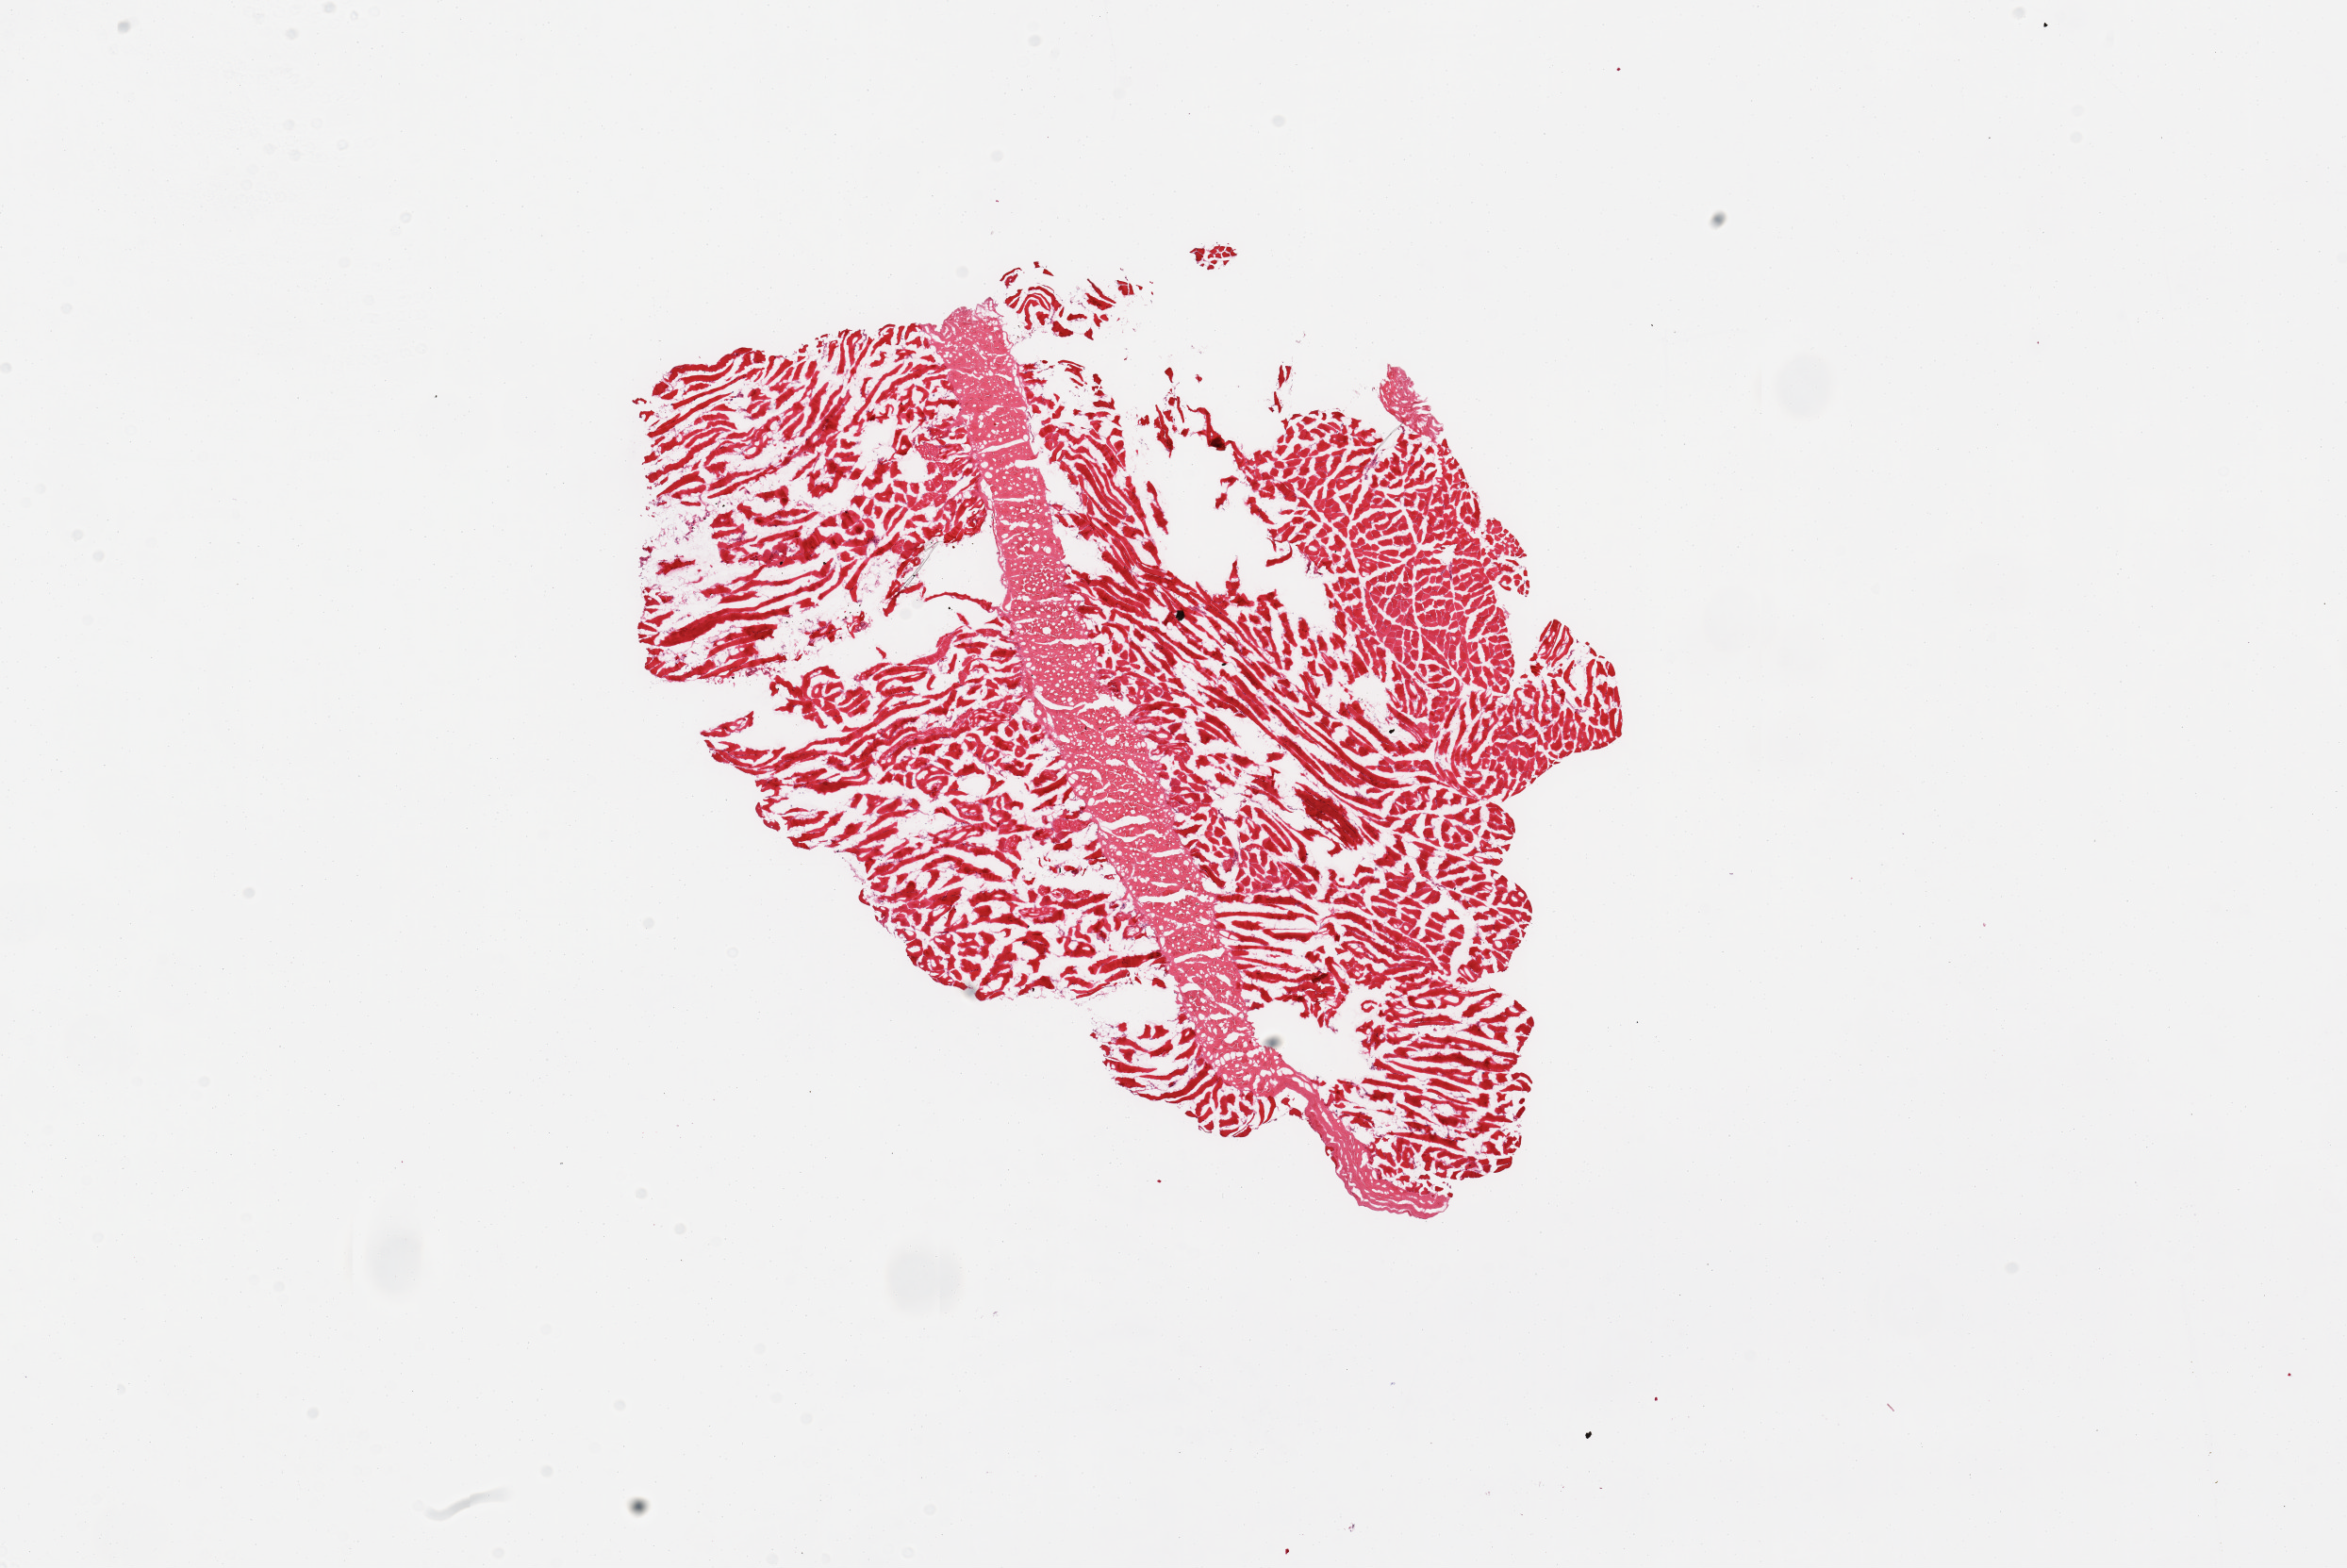
Hematoxylin and eosin (H&E) whole-slide image — shown as a low-resolution overview of the whole scanned area (about 19.7 x 13.2 mm). Donor: female.
Specimen: frozen section; sampled site (target tissue): skeletal muscle; tissue donor sample.